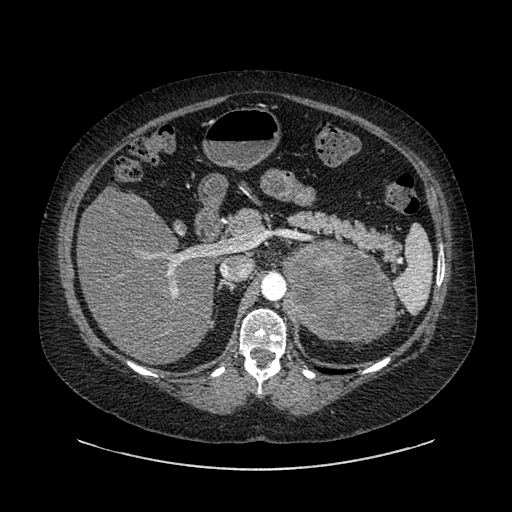
Contrast-enhanced abdominal CT, one axial slice; slice 573 of 769 in the series (ordered by position); 120 kVp; intravenous contrast given; soft-tissue window (W 400 / L 40 HU); 512 × 512 image matrix, field of view 460 × 460 mm. Female patient, age 61 years. Case-level facts recorded for this patient, not image findings: diagnosis: adrenocortical carcinoma; tumour side: left adrenal.
Outlined on this slice (semi-automatically segmented with operator editing):
- mass: bounding box (x1, y1, x2, y2) in pixels: (284, 241, 393, 341)